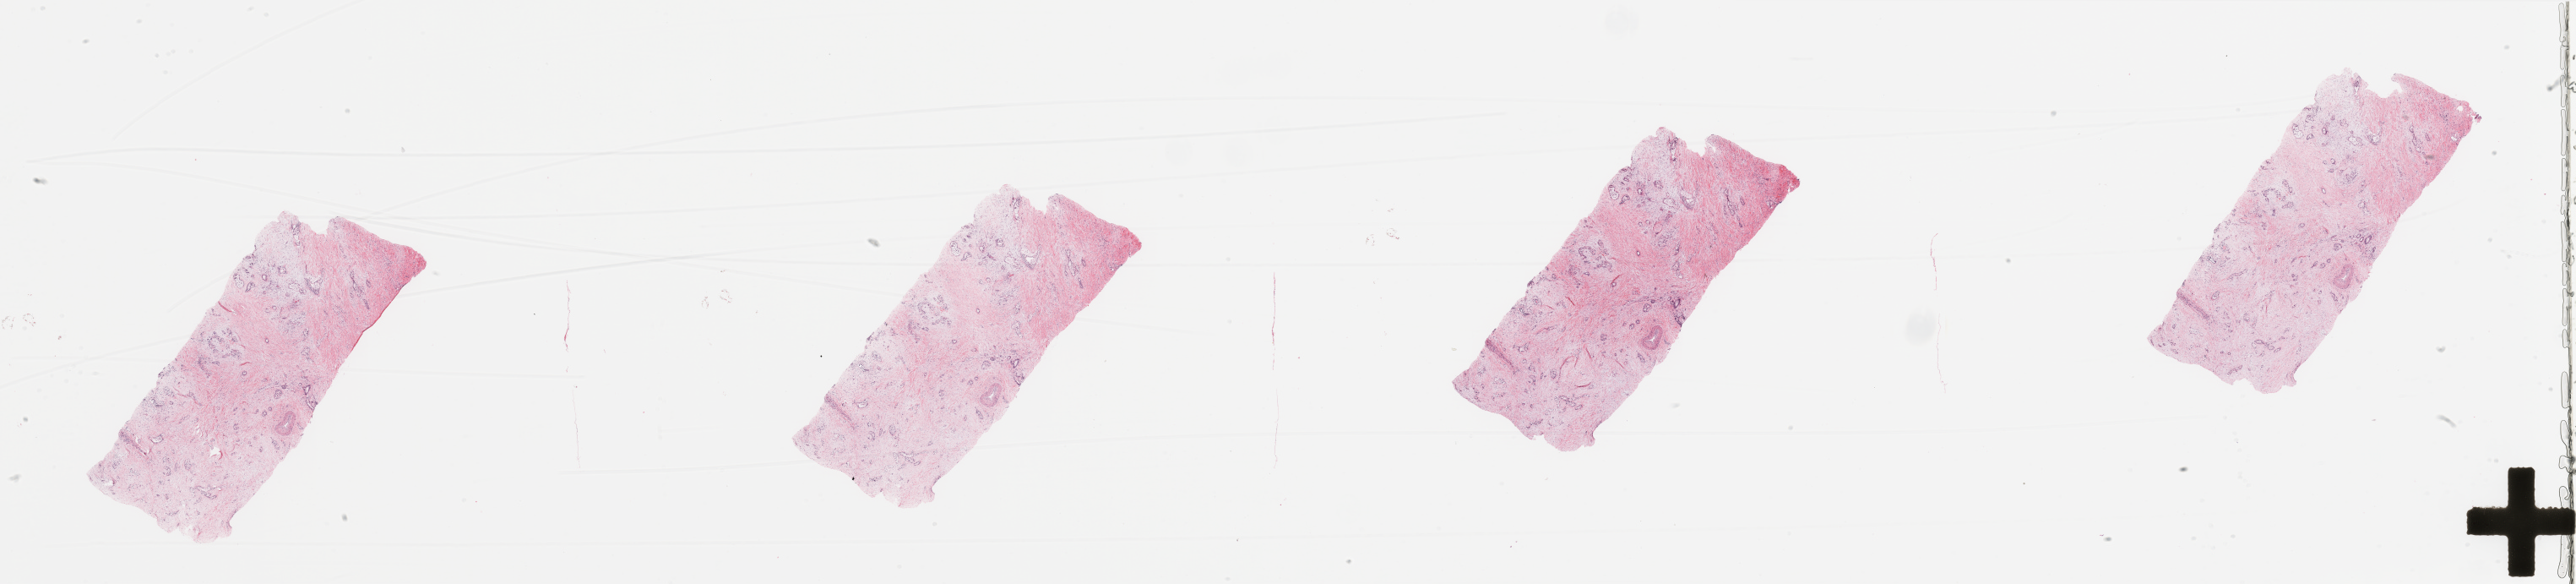
H&E whole-slide image — whole scanned area (about 48.2 x 10.9 mm) shown as a low-resolution overview. Tumour tissue sample, sampled site: pancreas. 63-year-old male patient. Histologic grade: G2 (moderately differentiated). Composition of this section per pathologist review: tumour nuclei 20%, necrosis 0%.
- AJCC pathologic stage: IB
- diagnosis: Infiltrating duct carcinoma, NOS
- primary tumour site (as recorded): tail